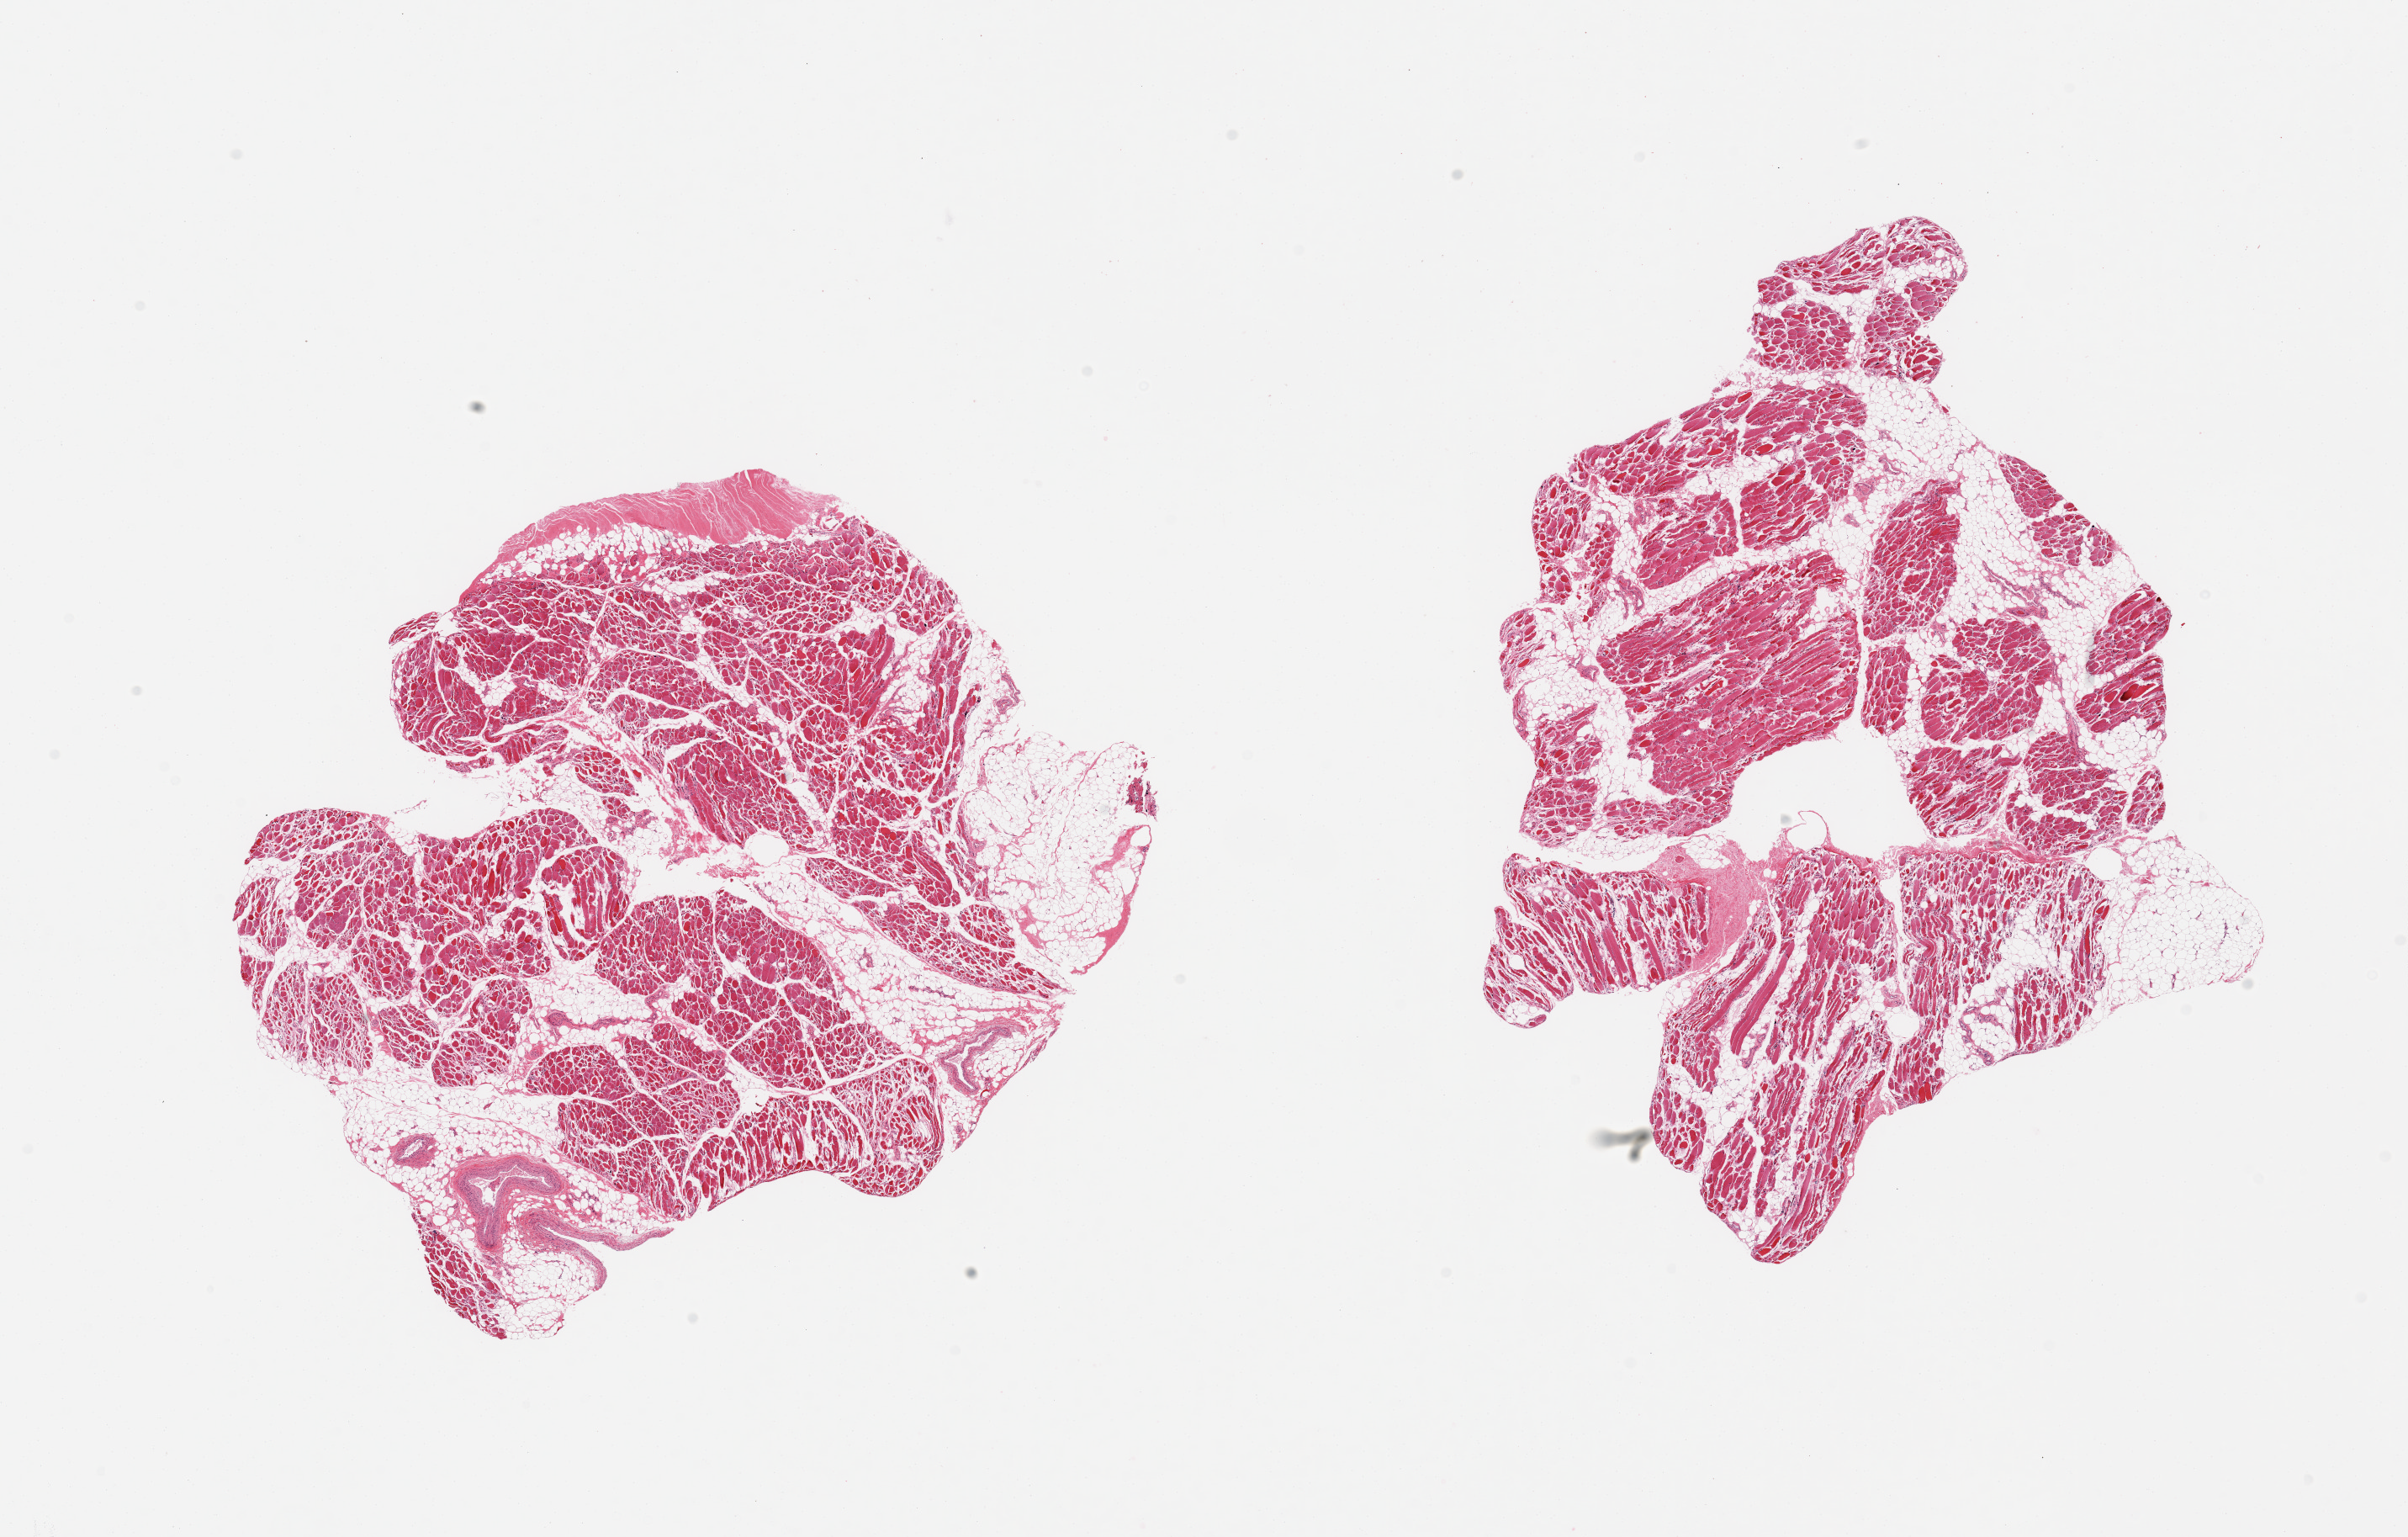
H&E whole-slide image, whole scanned area (about 22.6 x 14.4 mm) shown as a low-resolution overview. PAXgene-fixed paraffin-embedded (PFPE) section. Target tissue: skeletal muscle. Tissue donor sample. Male donor.
• reviewer comment on this tissue sample: 2 pieces; atrophy, includes 30 and 40% fat/tendon